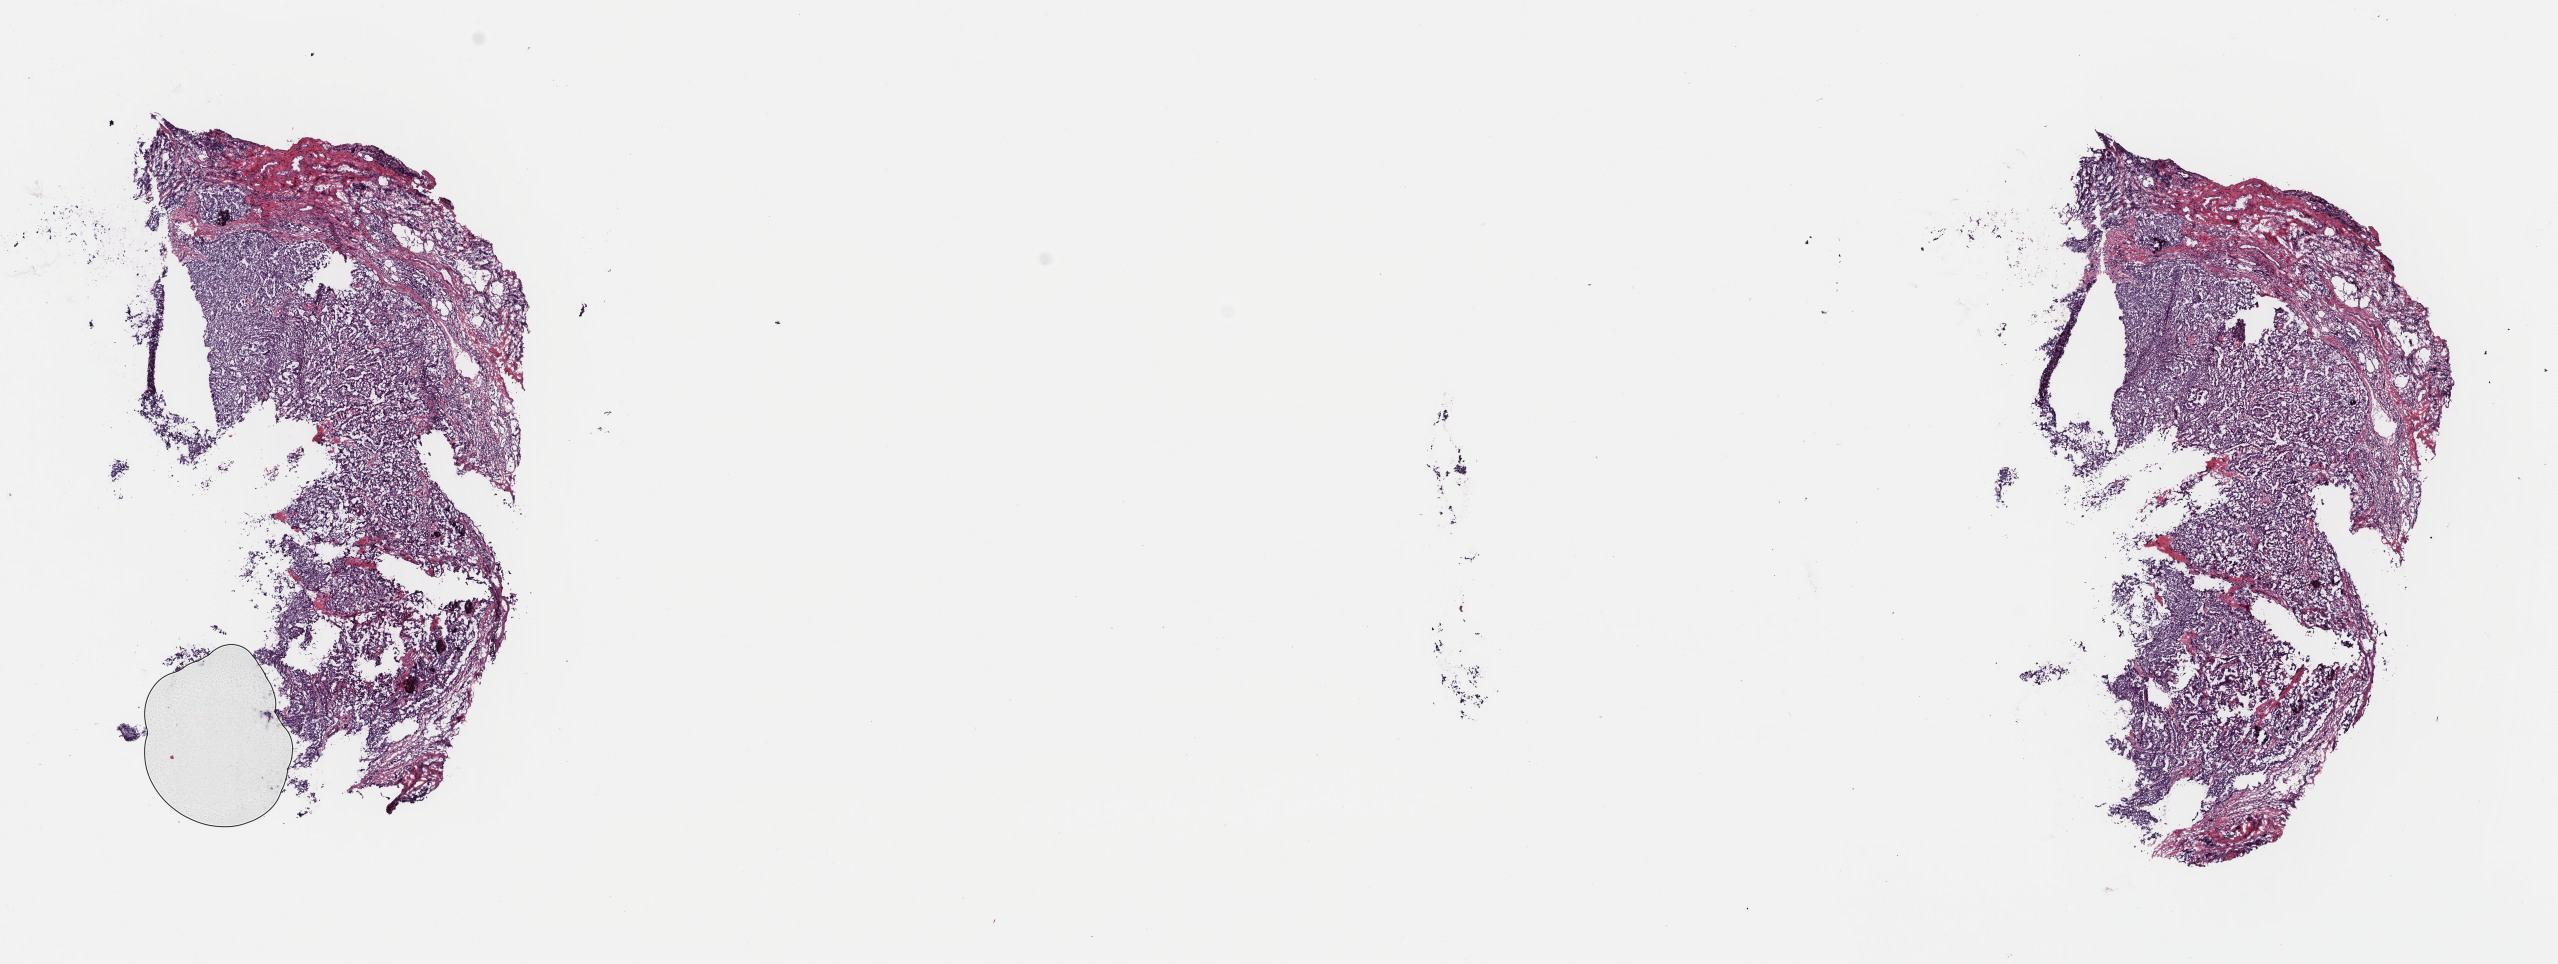
Whole-slide histology image, H&E, a low-resolution overview of the entire scanned area, about 20.2 x 7.6 mm; frozen section; thyroid, primary tumour sample. Female patient; age at initial diagnosis 32 years. Composition of this section per pathologist review: tumour cells 75%, tumour nuclei 75%, normal cells 2%, stromal cells 23%, necrosis 0%. Inflammatory infiltration, as recorded: lymphocyte infiltration 3%, monocyte infiltration 1%, neutrophil infiltration 1%.
AJCC pathologic stage: I. Histologic diagnosis: Papillary adenocarcinoma, NOS (thyroid gland). Laterality: right.